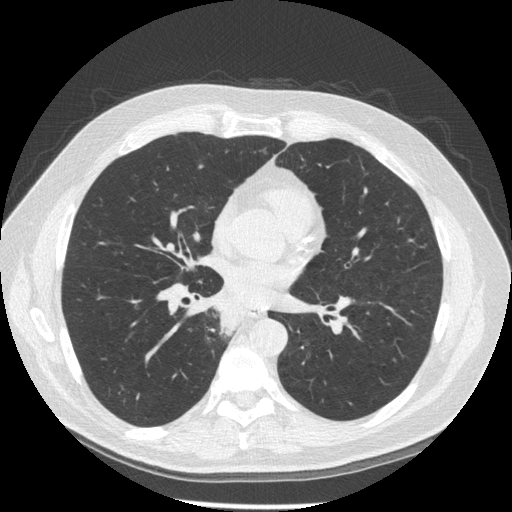
Low-dose screening chest CT, one axial slice; 120 kVp; lung window (W 1500 / L -600 HU); 1.25 mm slice thickness; 512 × 512 image matrix, field of view 370 × 370 mm.
Annotated regions visible in this slice (outlined manually by an expert reader):
- lesion 1 (tumor, lower lobe of right lung): bounding box (x1, y1, x2, y2) in pixels: (213, 303, 240, 338)